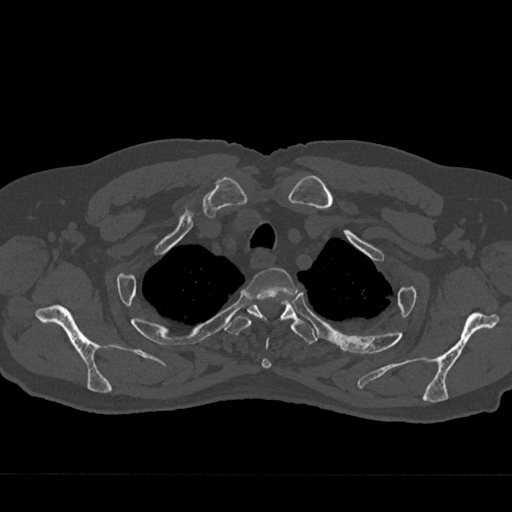
CT including the spine, one axial slice. Slice 588 of 797 in the series (ordered by position). Reconstruction kernel Br40s/3. Bone window (W 1800 / L 400 HU). 0.5 mm slice thickness. 512 × 512 image matrix, field of view 377 × 377 mm. Patient: male, 75 years. Case-level facts recorded for this patient, not image findings: primary cancer: renal.
Annotated regions visible in this slice (semi-automatic segmentation, software-assisted and operator-edited):
- T2 vertebra: box from (x=248, y=268) to (x=297, y=369) px
- T3 vertebra: (x=226, y=298)–(x=318, y=345)